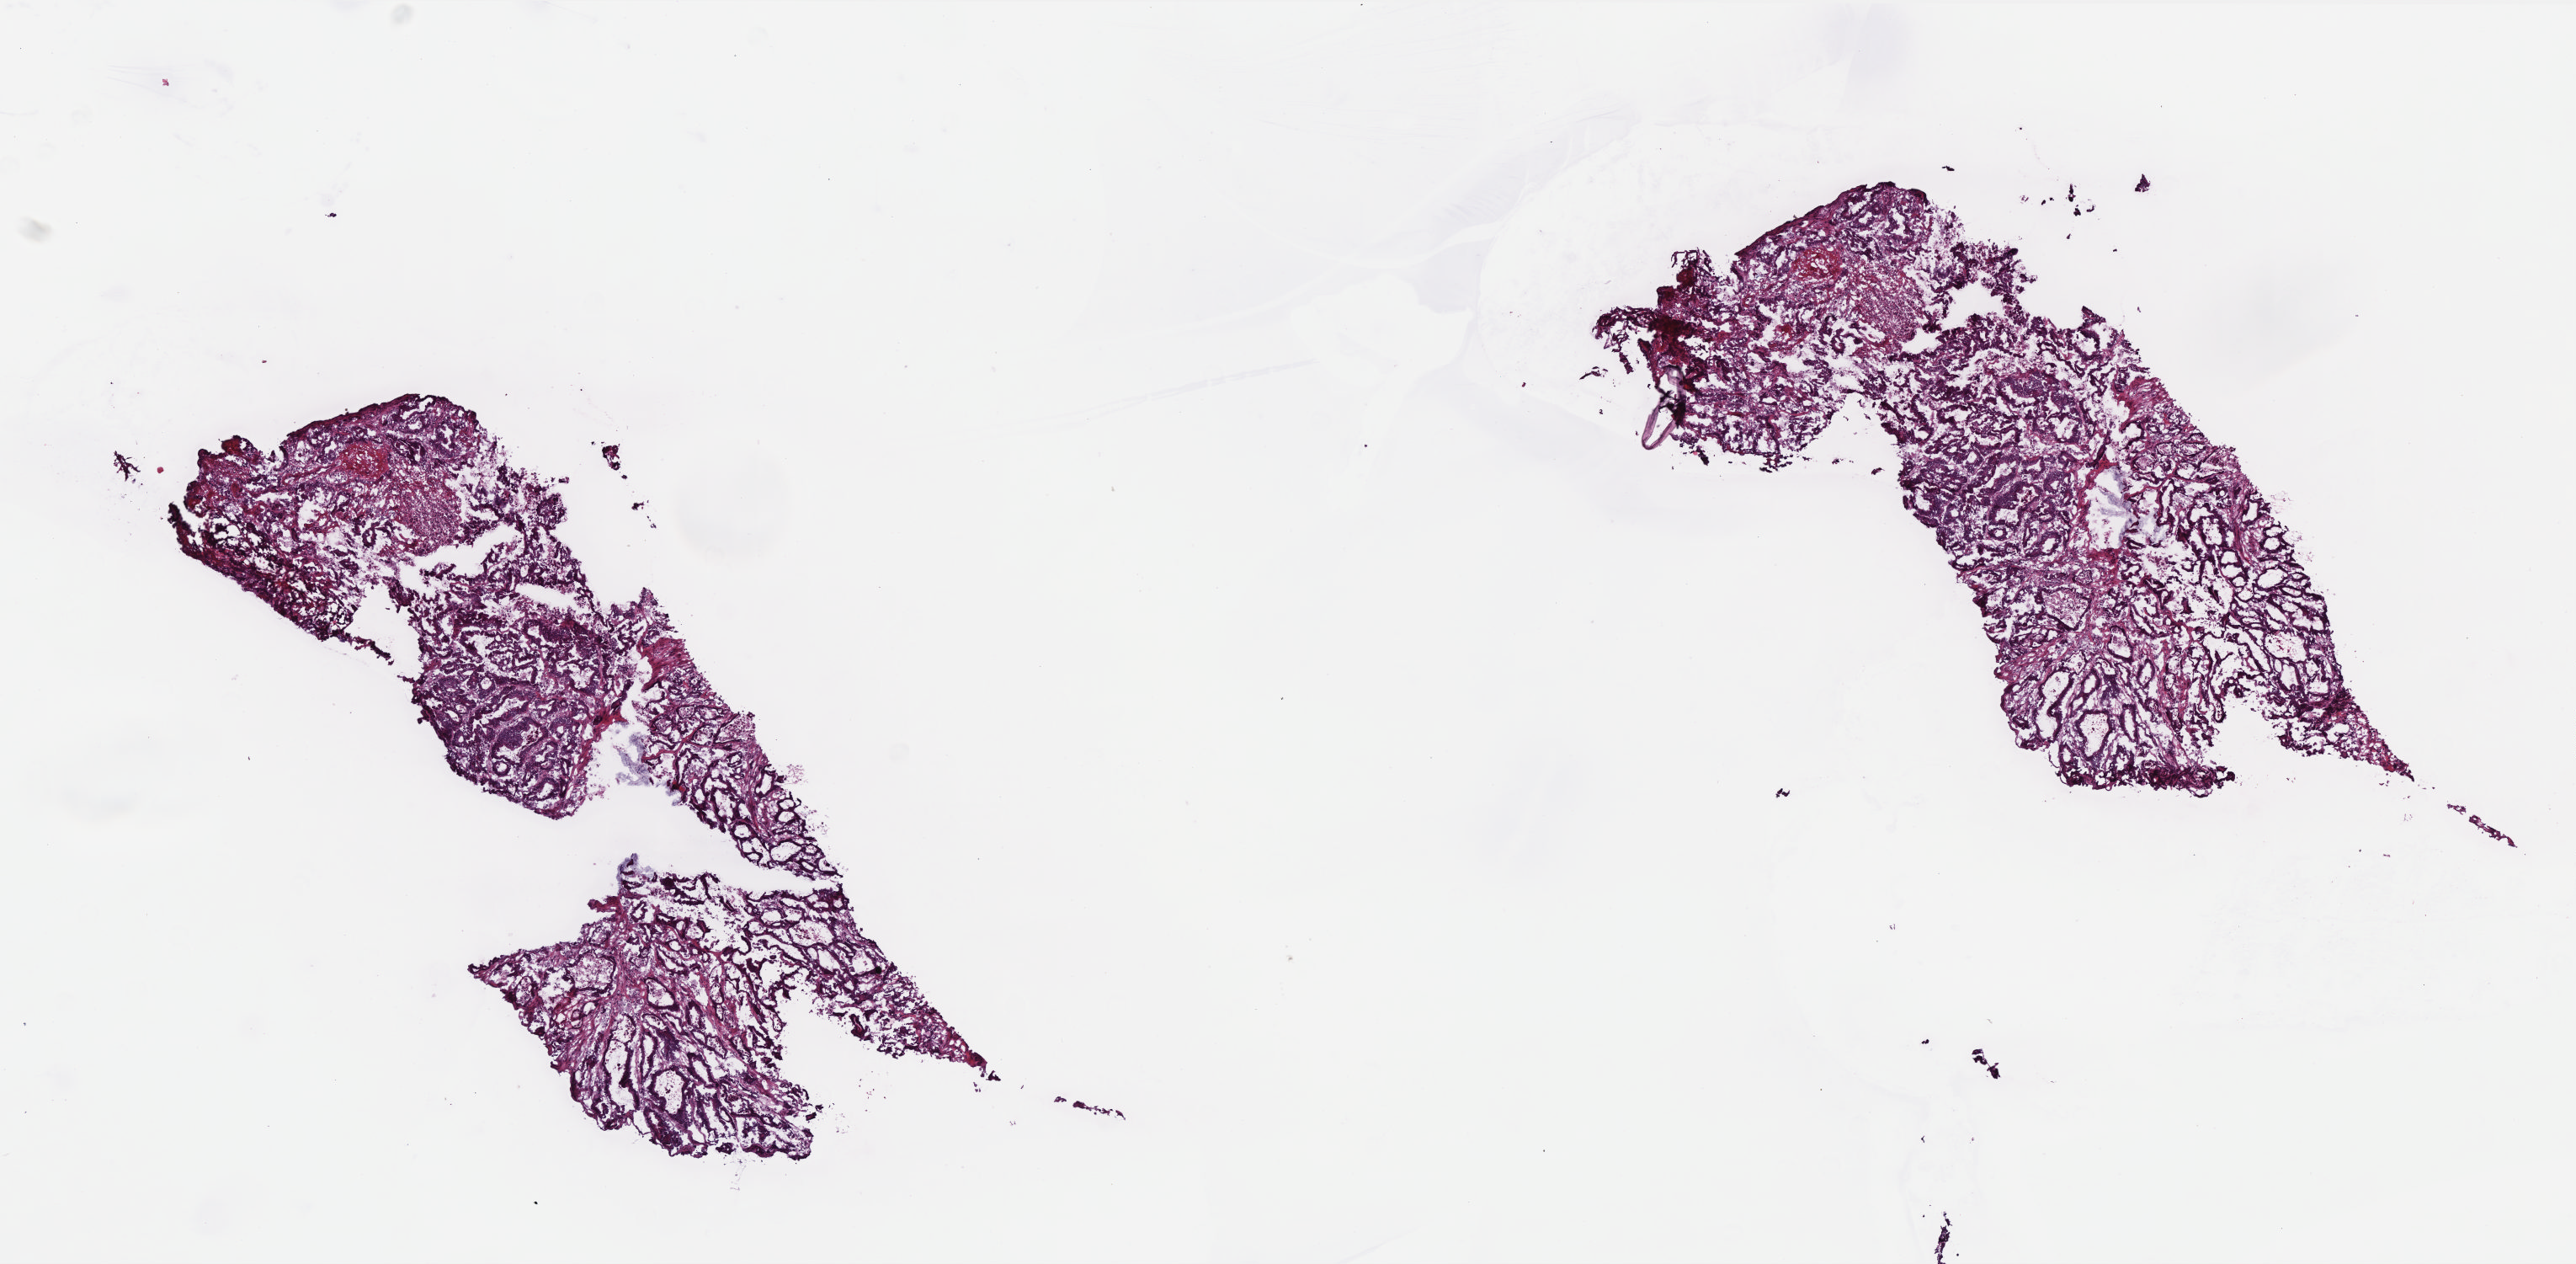
H&E-stained whole-slide image, a low-resolution overview of the entire scanned area, about 12.3 x 6.0 mm (acquisition: 40x scan), frozen section, primary tumour sample from the colon. Male, age 80 years at initial diagnosis. Slide review estimates, as recorded: tumour cells 90%, tumour nuclei 95%, normal cells 0%, stromal cells 5%, necrosis 5%. Inflammatory infiltration, as recorded: lymphocyte infiltration 1%, monocyte infiltration 1%, neutrophil infiltration 1%.
TNM: T3 N0 M0. Lymph nodes positive (case pathology): 0 of 34 examined. Histologic diagnosis: Adenocarcinoma, NOS (ascending colon). AJCC pathologic stage: IIA (6th edition).